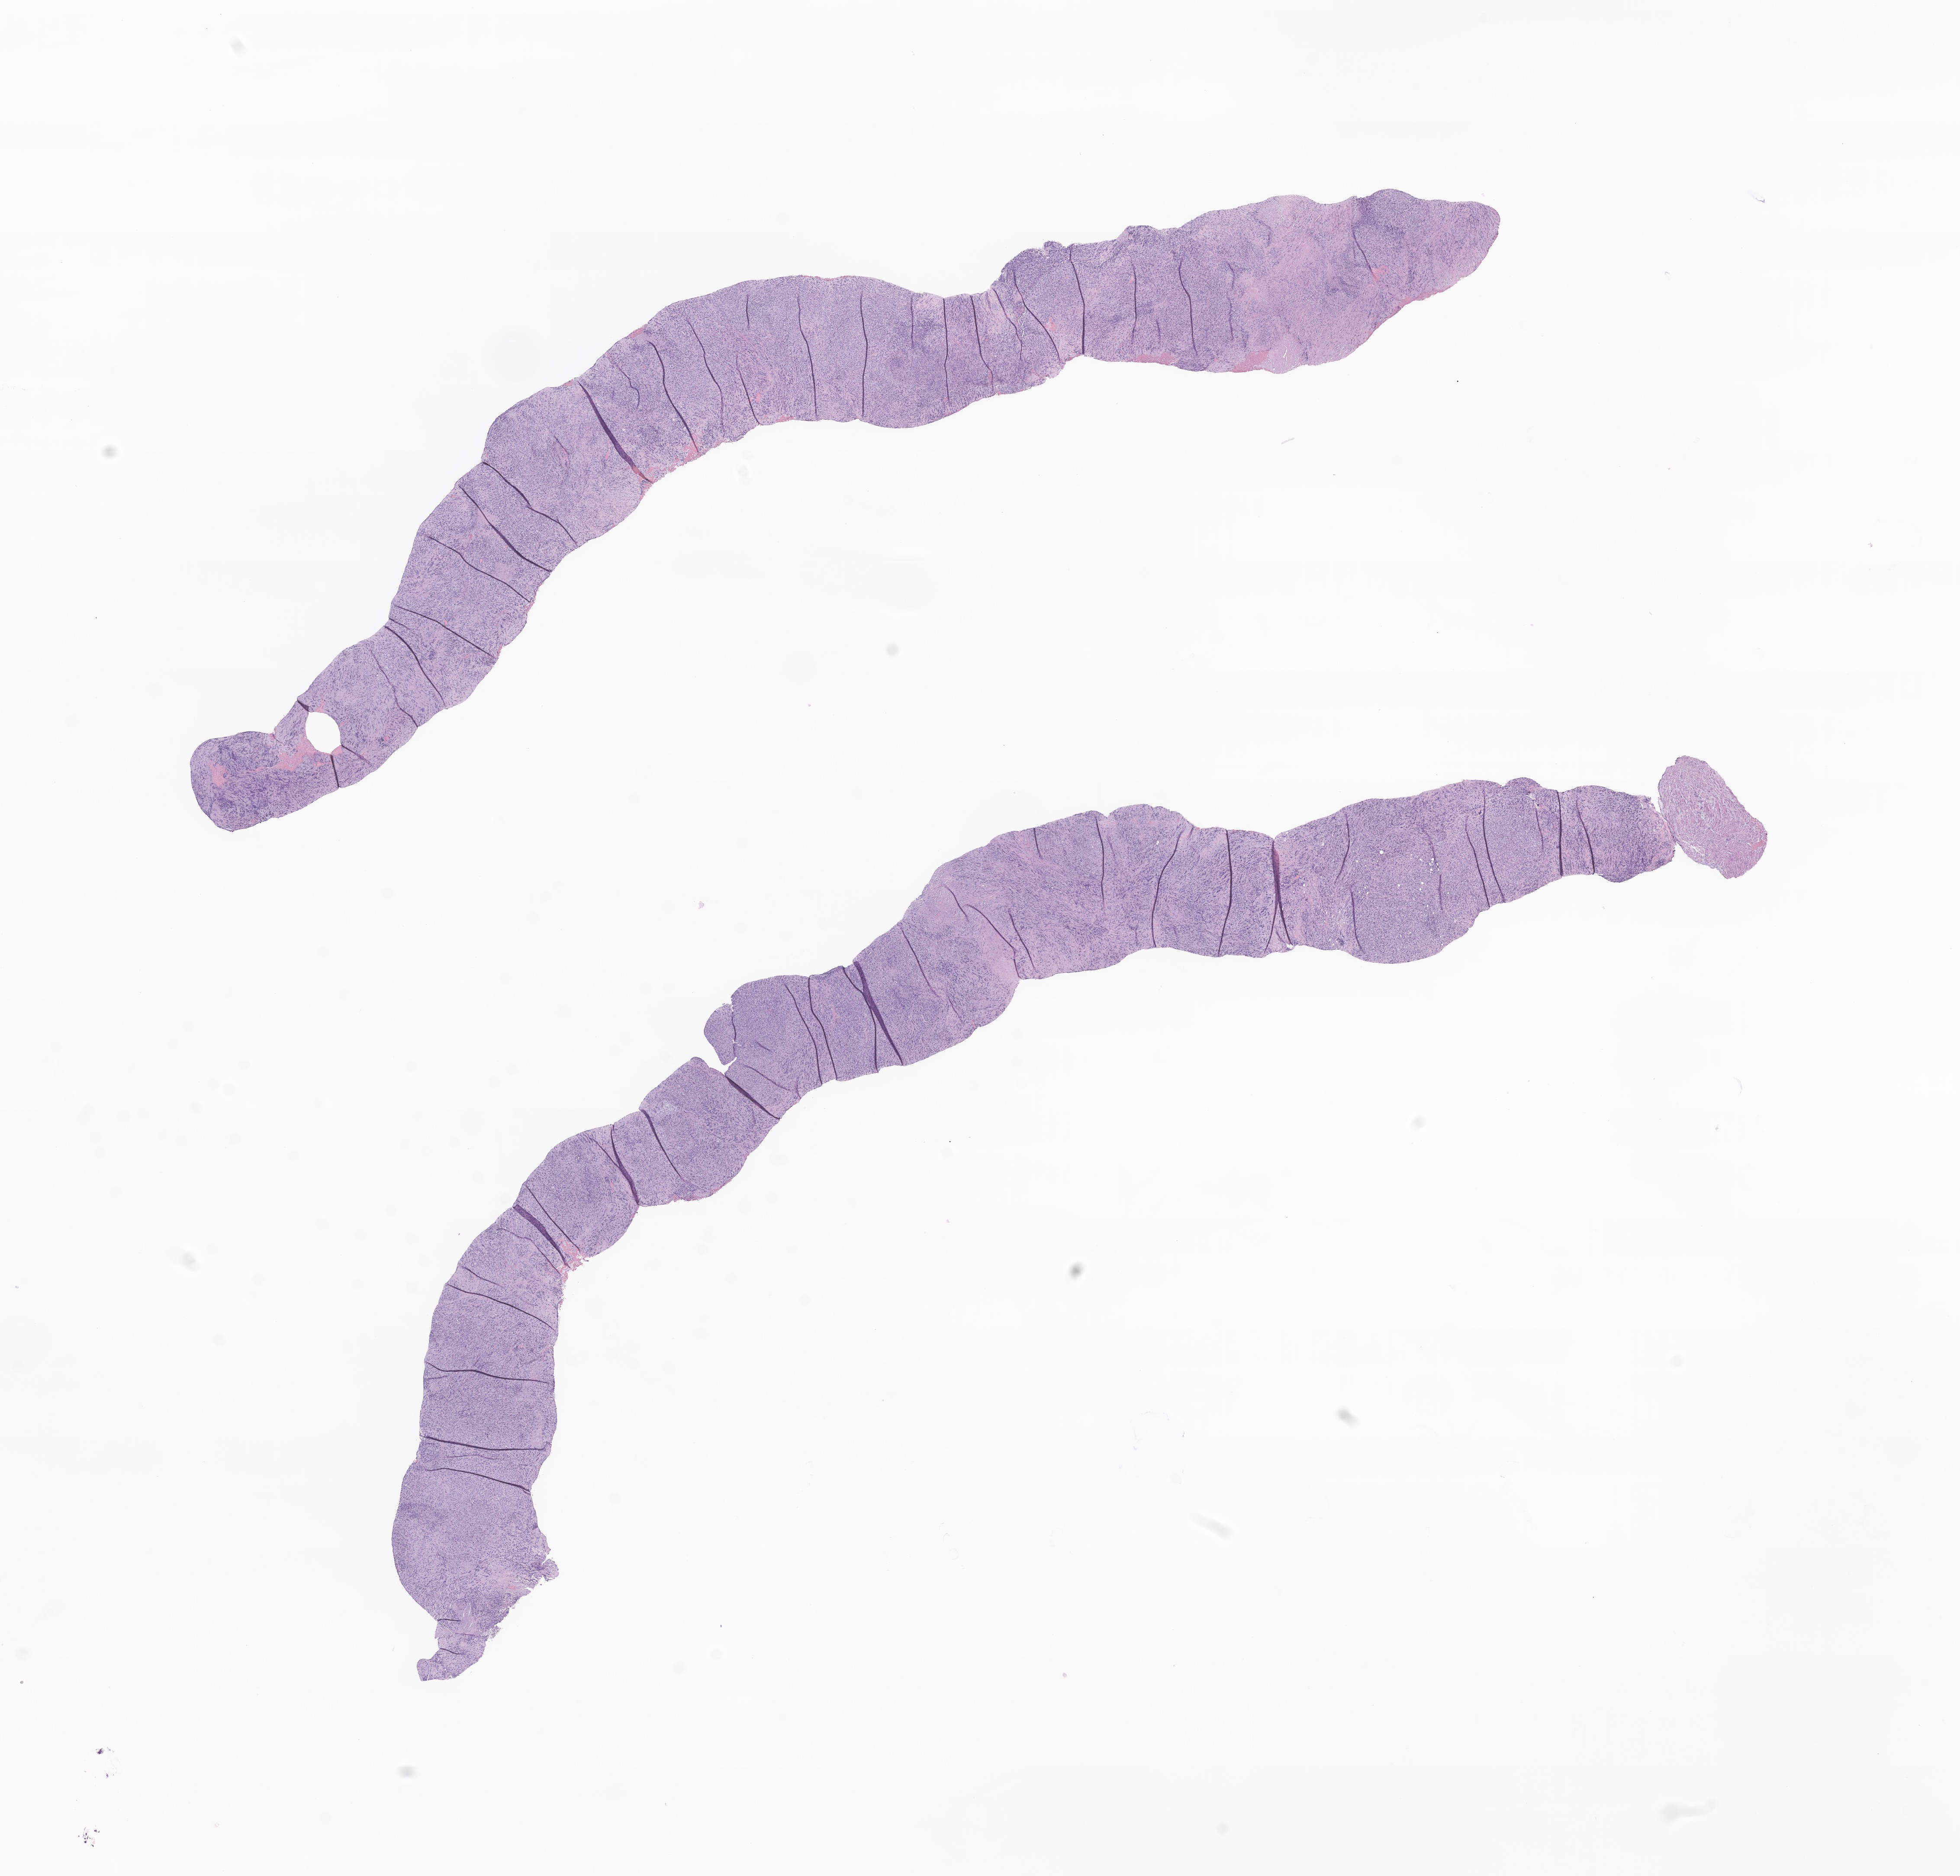
H&E whole-slide image of tumor tissue from the maxillary sinus — whole scanned area (about 19.1 x 18.3 mm) shown as a low-resolution overview. Formalin-fixed paraffin-embedded section. Patient: male, age 121 months (10 years 1 month).
Diagnosis (ICD-O-3 morphology term): Spindle cell rhabdomyosarcoma.